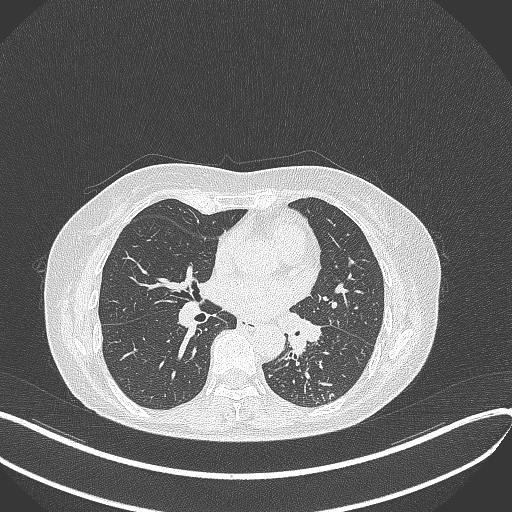
Chest CT, one axial slice. Slice 204 of 429 in the series (ordered by position). Reconstruction kernel B70f. 100 kVp. Lung window (W 1500 / L -600 HU). 512 × 512 image matrix, field of view 400 × 400 mm. Patient: female, 63 years. From the clinical record (not read from this slice): clinical TNM (as recorded): T1b N0 M0; histopathological grade: G2-3.
Structures marked on this image (bounding box drawn by a radiologist):
- lung tumour (recorded histology: adenocarcinoma): bounding box (x1, y1, x2, y2) in pixels: (281, 309, 323, 361)